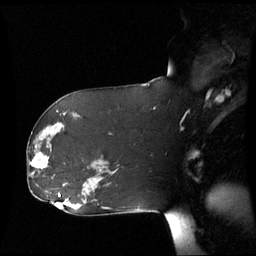
Breast MRI (dynamic contrast-enhanced), one sagittal slice; position 34 of 60 along the scan axis; dynamic contrast-enhanced series, image 2 of 3 at this slice position (ordered by acquisition); 1.5 T; TE 4.2 ms, TR 8.9 ms; 256 × 256 image matrix, field of view 280 × 280 mm. Patient: female, 61 years. Case-level facts recorded for this patient, not image findings: setting: breast cancer imaged before/during neoadjuvant chemotherapy; receptor status: HR-positive, HER2-negative.
Structures marked on this image (semi-automatically segmented with operator editing):
- analysis volume of interest (the breast-tissue region the enhancement analysis was run in; not a lesion): box from (x=28, y=142) to (x=53, y=177) px
- tumour enhancement mask (voxels above the 70 % enhancement threshold inside the analysis volume of interest): (x=32, y=152)–(x=49, y=169)